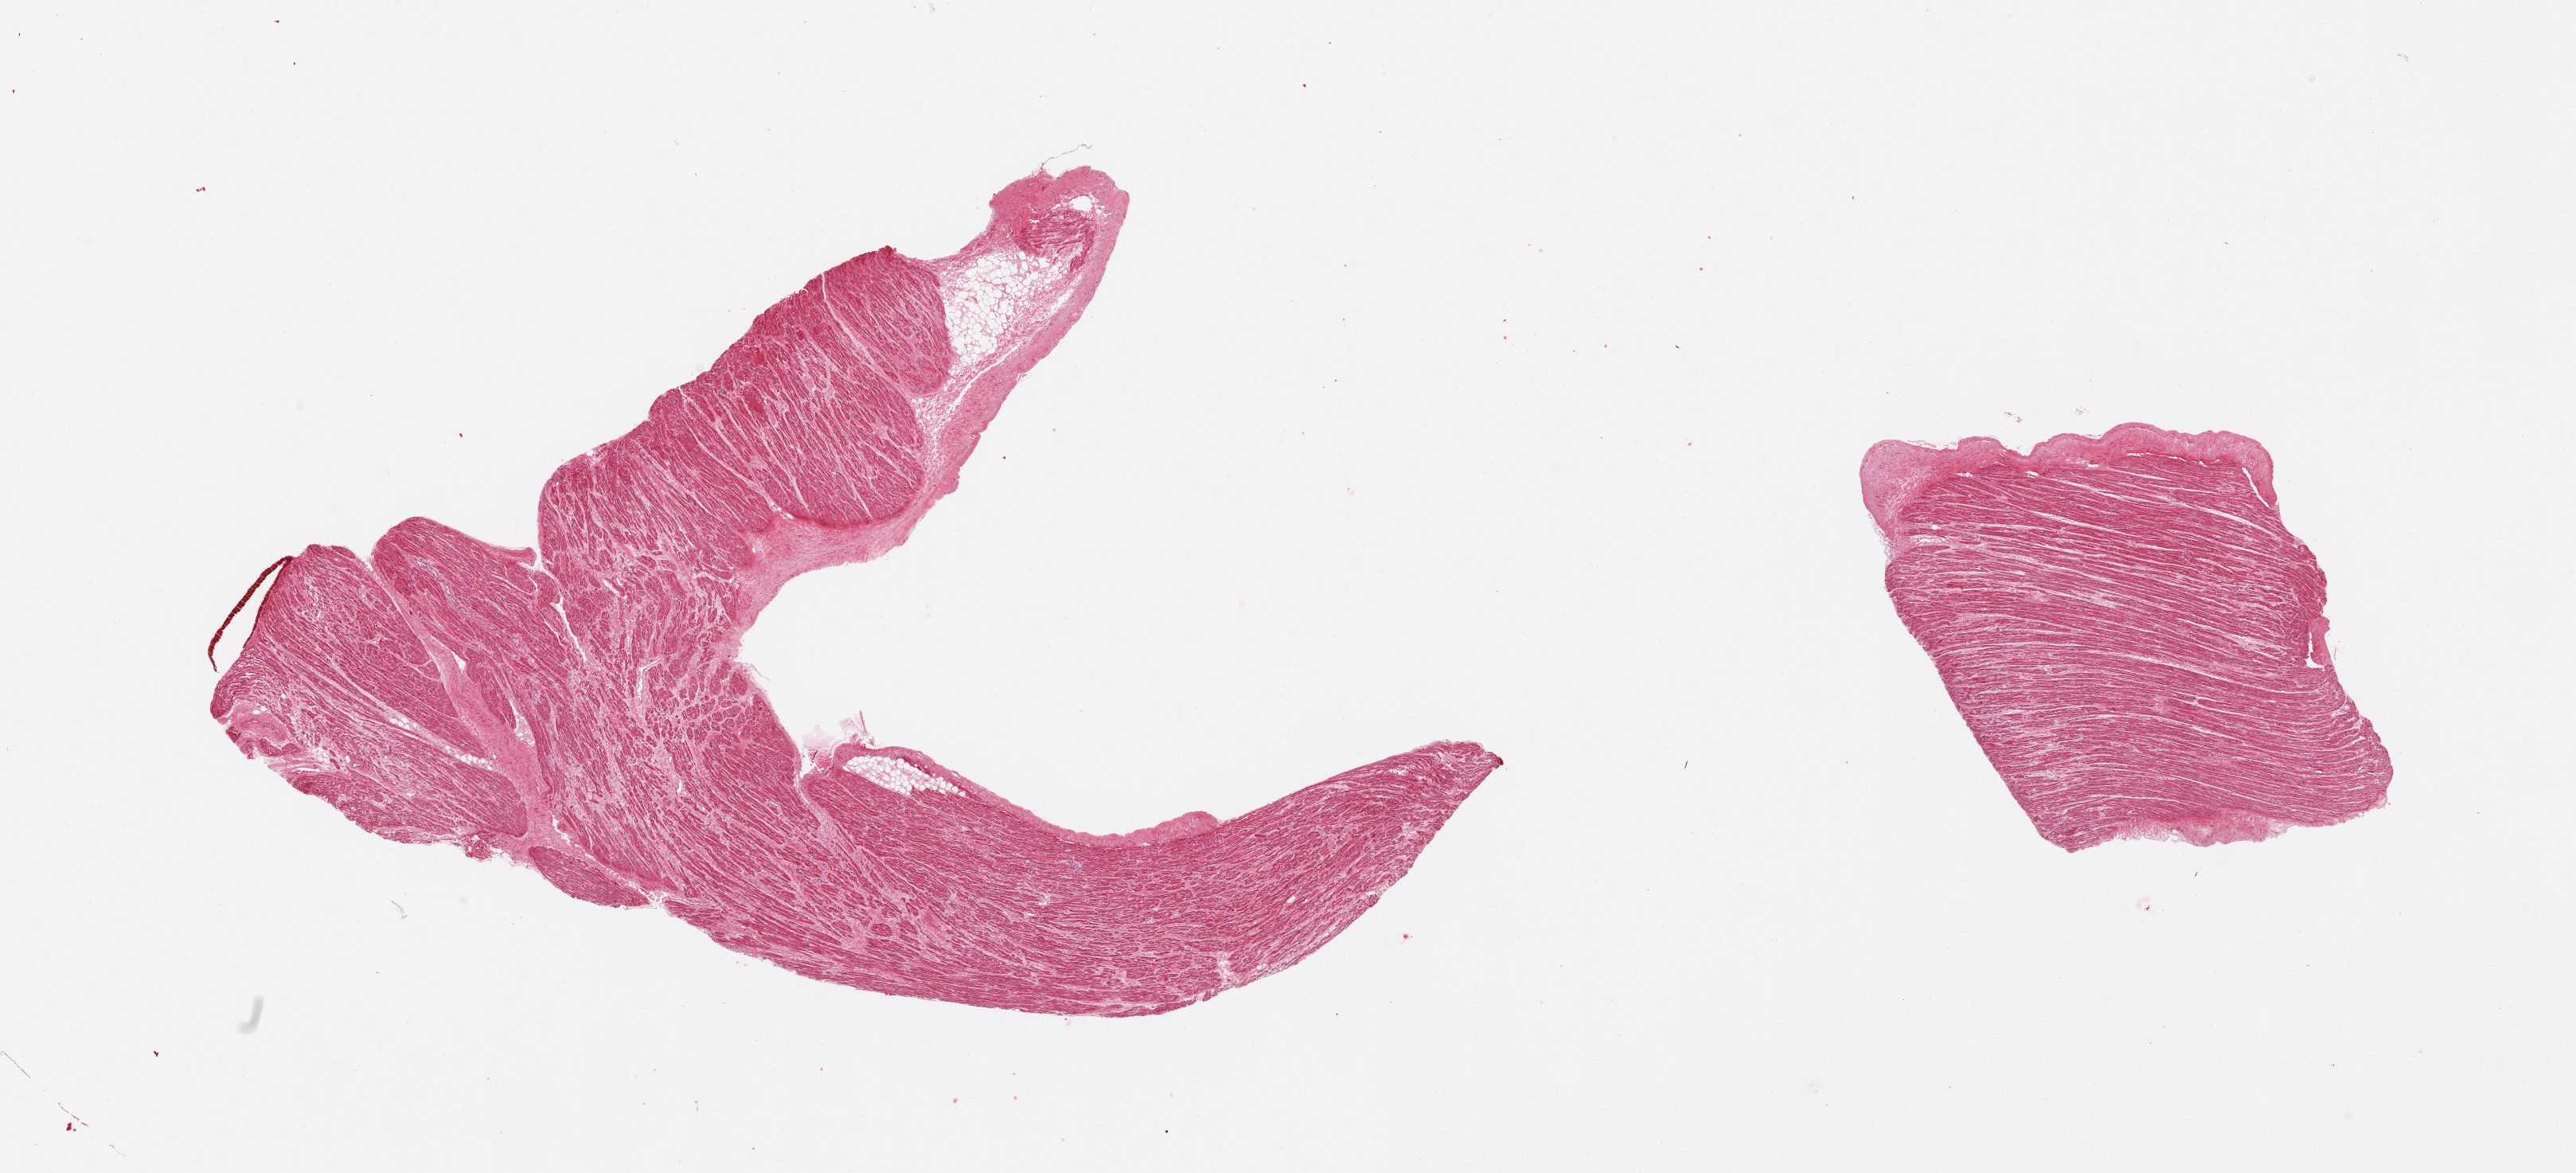
Hematoxylin and eosin (H&E) whole-slide image, a low-resolution overview of the entire scanned area, about 25.6 x 11.7 mm (slide scanned at 20x); PAXgene-fixed, paraffin-embedded tissue; target tissue: auricular appendage; tissue donor sample. Male donor.
Review note (as recorded): 2 pieces; 10% fat & fibrous in 1.